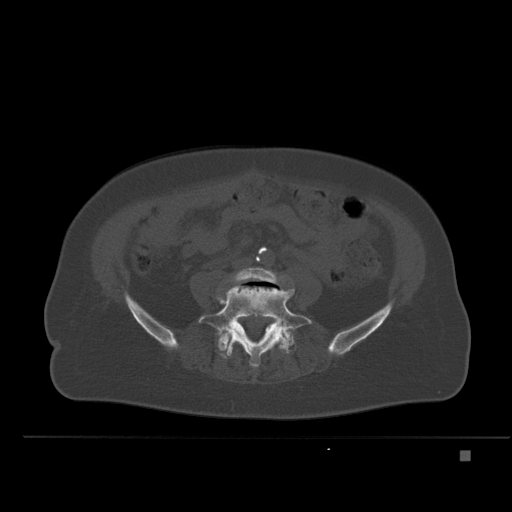
CT including the spine, one axial slice; position 164 of 477 along the scan axis; bone window (W 1800 / L 400 HU); 1.5 mm slice thickness; 512 × 512 image matrix, field of view 422 × 422 mm. Female patient, age 74 years. From the clinical record (not read from this slice): primary cancer: colon.
Annotated regions visible in this slice (semi-automatic segmentation, software-assisted and operator-edited):
- L4 vertebra: box from (x=231, y=267) to (x=281, y=284) px
- L5 vertebra: (x=198, y=287)–(x=312, y=368)